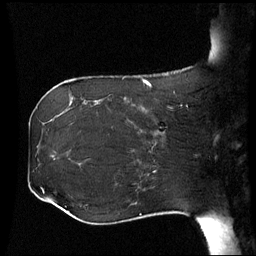
Breast MRI (dynamic contrast-enhanced), one sagittal slice; slice 20 of 60 in the series (ordered by position); dynamic contrast-enhanced series, image 2 of 3 at this slice position (ordered by acquisition); 1.5 T; TE 4.2 ms, TR 8.9 ms; 2.5 mm slice thickness; 256 × 256 image matrix, field of view 230 × 230 mm. Female patient, age 42 years. From the clinical record (not read from this slice): setting: breast cancer imaged before/during neoadjuvant chemotherapy; receptor status: HER2-positive.
Annotated regions visible in this slice (semi-automatic segmentation, software-assisted and operator-edited):
- analysis volume of interest (the breast-tissue region the enhancement analysis was run in; not a lesion): box from (x=106, y=102) to (x=173, y=150) px
- tumour enhancement mask (voxels above the 70 % enhancement threshold inside the analysis volume of interest): (x=136, y=107)–(x=142, y=133)